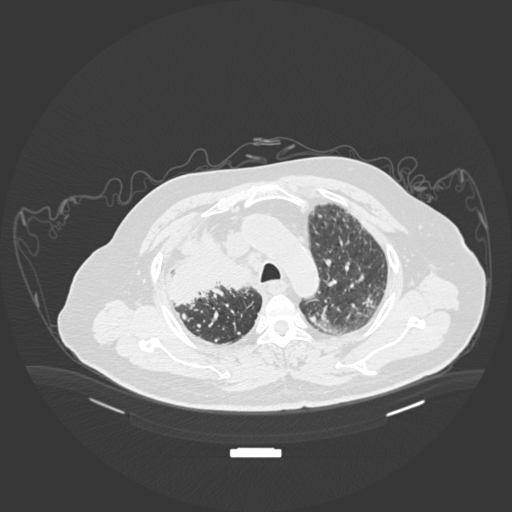
Chest CT, one axial slice. Position 142 of 201 along the scan axis. Reconstruction kernel B30f. 120 kVp. Lung window (W 1500 / L -600 HU). 512 × 512 image matrix, field of view 500 × 500 mm. Male patient, age 69 years. Case-level facts recorded for this patient, not image findings: clinical TNM (as recorded): T4 N3 M1.
Structures marked on this image (bounding box drawn by a radiologist):
- lung tumour (recorded histology: adenocarcinoma): bounding box (x1, y1, x2, y2) in pixels: (169, 220, 263, 305)